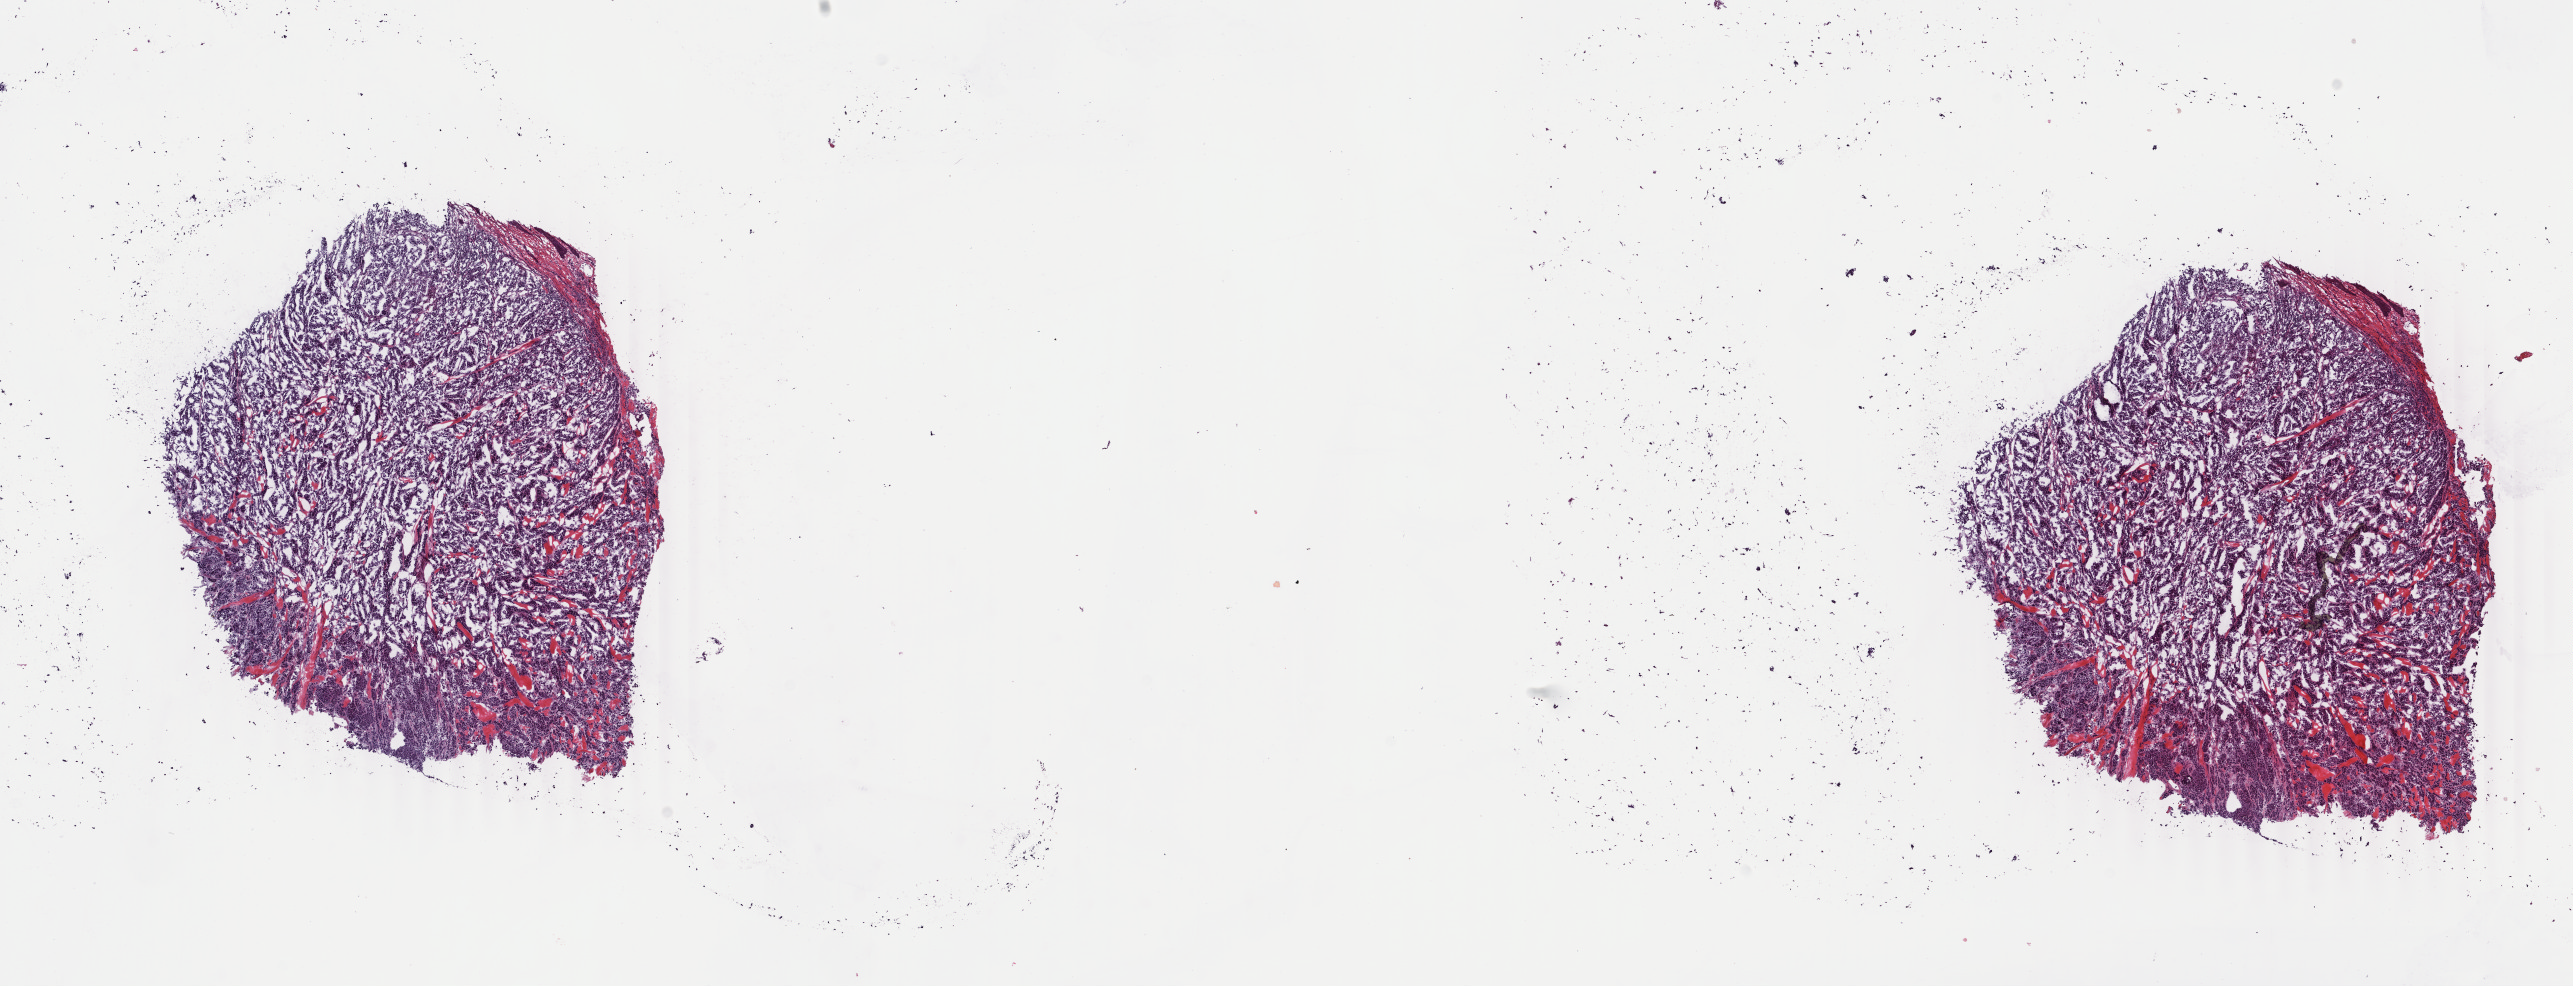
H&E-stained whole-slide image — low-resolution overview of the scanned area, about 20.5 x 7.8 mm (slide scanned at 40x); frozen section from the top of the tissue portion; skin, primary tumour sample. Female patient; age at initial diagnosis 65 years. Pathologist review of this section (percent, as recorded): tumour cells 100%, tumour nuclei 80%, normal cells 0%, stromal cells 0%, necrosis 0%. Inflammatory infiltration, as recorded: lymphocyte infiltration 1%, monocyte infiltration 0%, neutrophil infiltration 0%.
Diagnosis: Malignant melanoma, NOS.